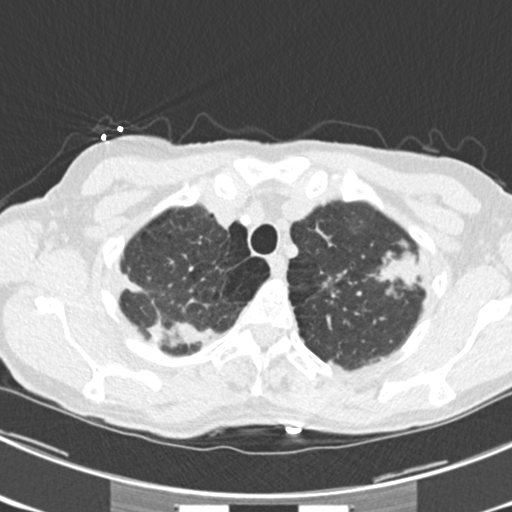
Low-dose screening chest CT, axial slice; third screening round (two years after baseline); lung window (W 1500 / L -600 HU); 2 mm slice thickness; standard (soft-tissue) reconstruction kernel (B30f). Female participant, aged 63 years at enrolment. Current smoker at enrolment.
Expert reader's lesion annotation, box from (x=373, y=240) to (x=439, y=303) px. The screening reader recorded 9 non-calcified nodules or masses ≥4 mm on this exam (left upper lobe, right upper lobe, left upper lobe, left lower lobe, right middle lobe, left lower lobe, left lower lobe, right lower lobe, right lower lobe); which of them this box marks is not recorded. Official screen result: positive, other. Later outcome: lung cancer diagnosed 15 days after this screen — bronchiolo-alveolar adenocarcinoma, NOS, right upper lobe, right middle lobe, right lower lobe, left upper lobe, left lower lobe, moderately differentiated (G2), stage IV (AJCC 6th edition).